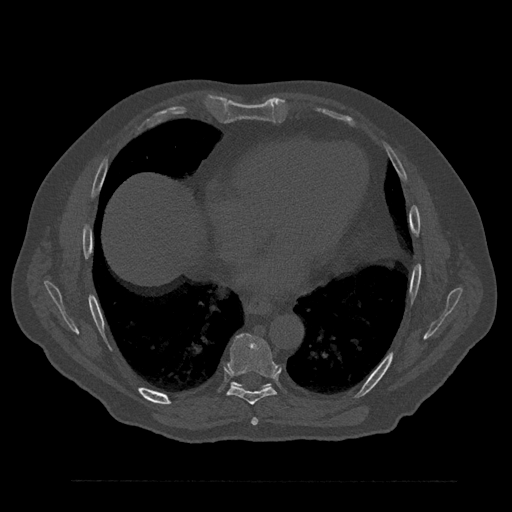
CT including the spine, one axial slice; 120 kVp; bone window (W 1800 / L 400 HU); 0.5 mm slice thickness; 512 × 512 image matrix. Male patient, age 61 years. From the clinical record (not read from this slice): primary cancer: prostate.
Outlined on this slice (semi-automatic segmentation, software-assisted and operator-edited):
- T7 vertebra: bounding box (x1, y1, x2, y2) in pixels: (252, 417, 258, 425)
- T8 vertebra: (227, 334, 278, 405)
- T9 vertebra: (232, 382, 270, 387)